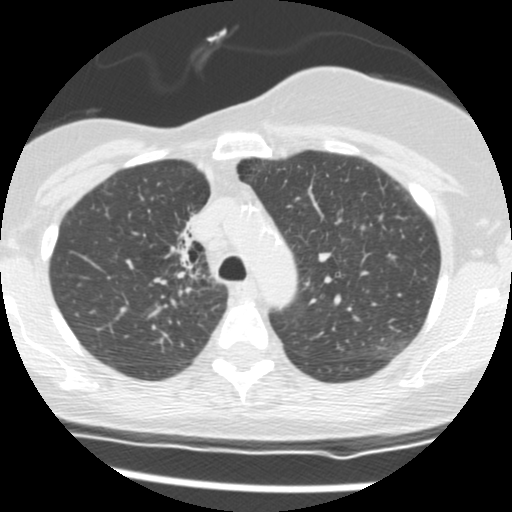
Axial slice from a low-dose chest CT screening exam. Second screening round (one year after baseline). Lung window (W 1500 / L -600 HU). Standard (soft-tissue) reconstruction kernel (STANDARD). Slice 35 of 165 in the series. Female, age 56 years at enrolment.
Expert-annotated lung lesion, bounding box <155,206,215,280> (left, top, right, bottom; pixels). The screening reader recorded 2 non-calcified nodules or masses ≥4 mm on this exam (right middle lobe, right lower lobe); which of them this box marks is not recorded. Official screen result: positive, change unspecified: nodule(s) >= 4 mm or enlarging nodule(s), mass(es), or other non-specific abnormalities suspicious for lung cancer. Lung cancer was diagnosed 675 days after this screen: adenocarcinoma, NOS, right upper lobe, stage IIIB (AJCC 6th edition), 8 mm at pathology.